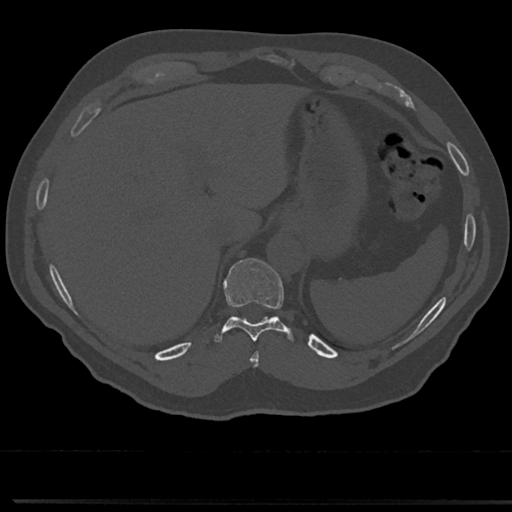
CT including the spine, one axial slice. Position 253 of 817 along the scan axis. Bone window (W 1800 / L 400 HU). 512 × 512 image matrix, field of view 355 × 355 mm. Male patient, age 61 years. From the clinical record (not read from this slice): primary cancer: prostate.
Structures marked on this image (semi-automatically segmented with operator editing):
- T10 vertebra: bounding box (x1, y1, x2, y2) in pixels: (211, 259, 298, 345)
- T9 vertebra: (251, 347, 260, 368)